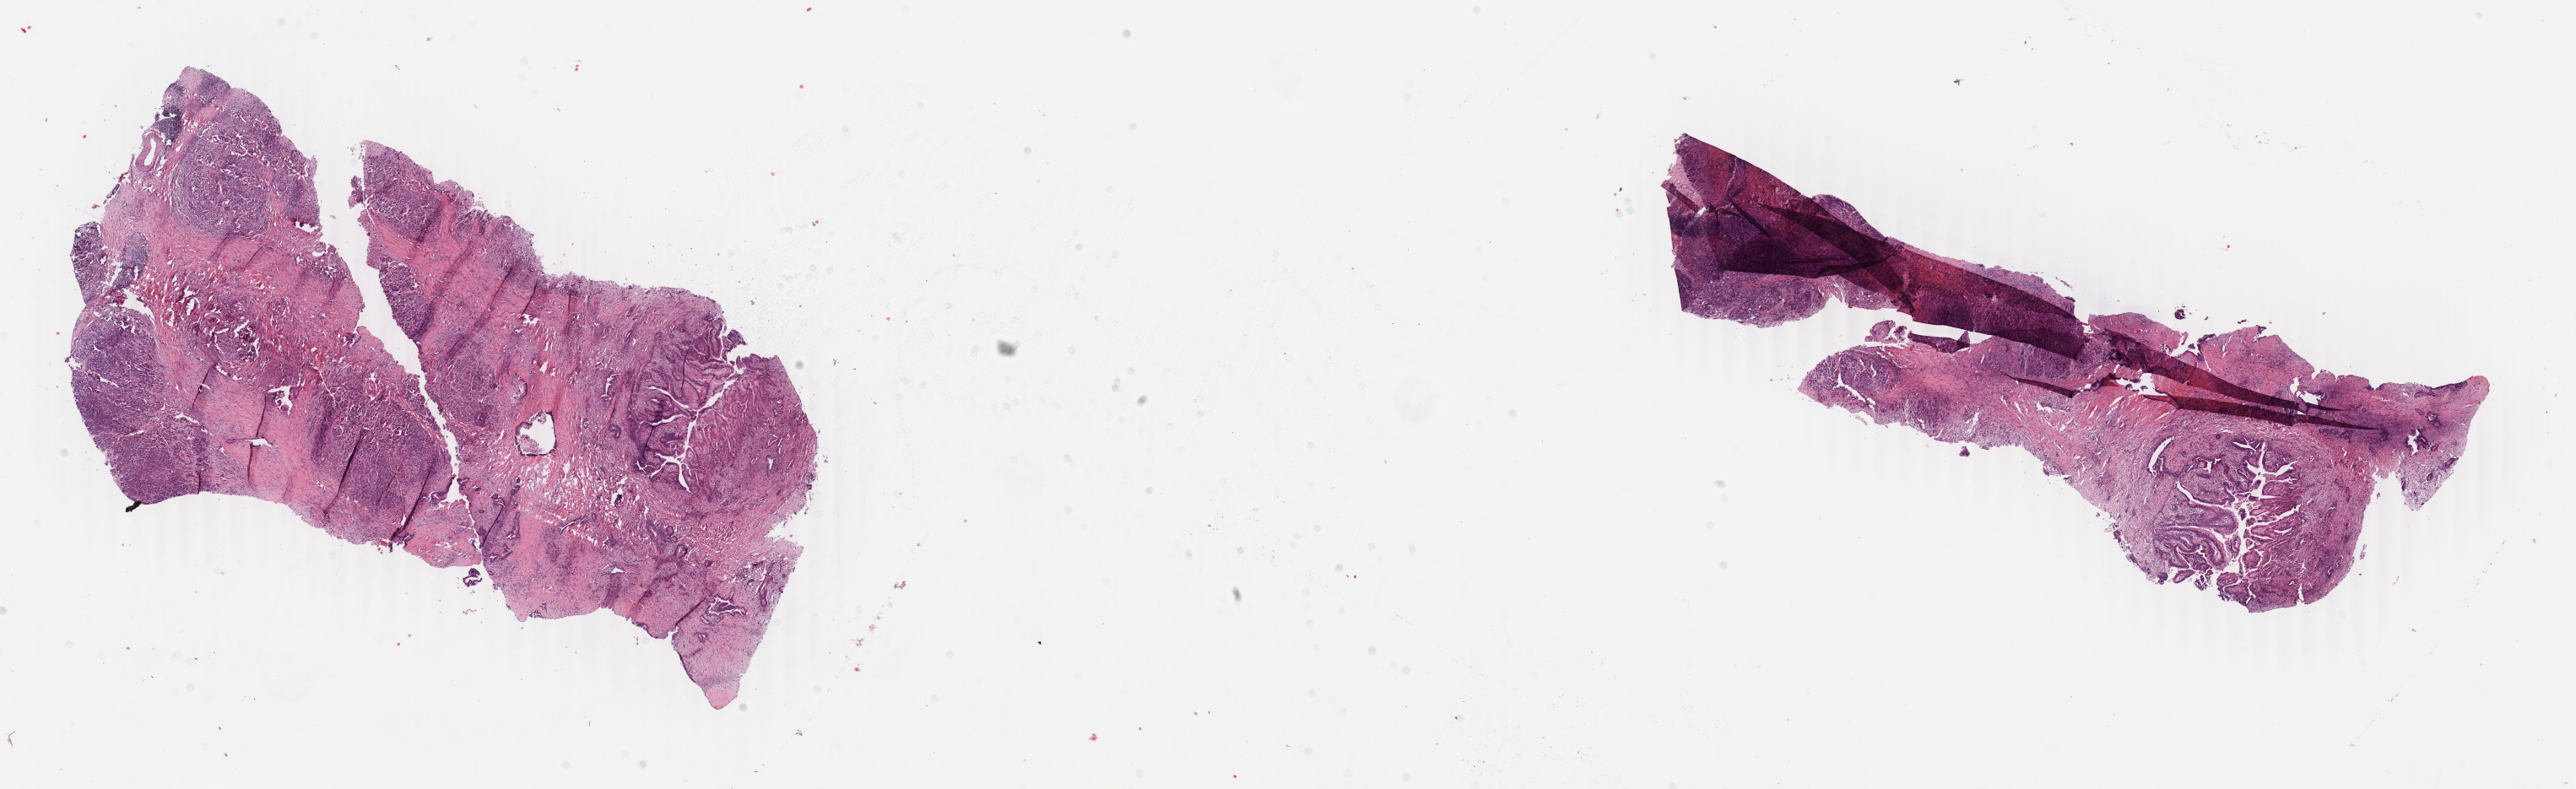
H&E-stained whole-slide image, low-resolution overview of the scanned area, about 24.3 x 7.4 mm (from a 40x scan), formalin-fixed paraffin-embedded (FFPE) diagnostic section, primary tumour sample from the pancreas. Male, age 53 years at initial diagnosis. Histologic grade: G2 (moderately differentiated).
AJCC pathologic stage: IIA (7th edition). Diagnosis: Adenocarcinoma, NOS (head of pancreas). Lymph nodes positive (case pathology): 0 of 21 examined.